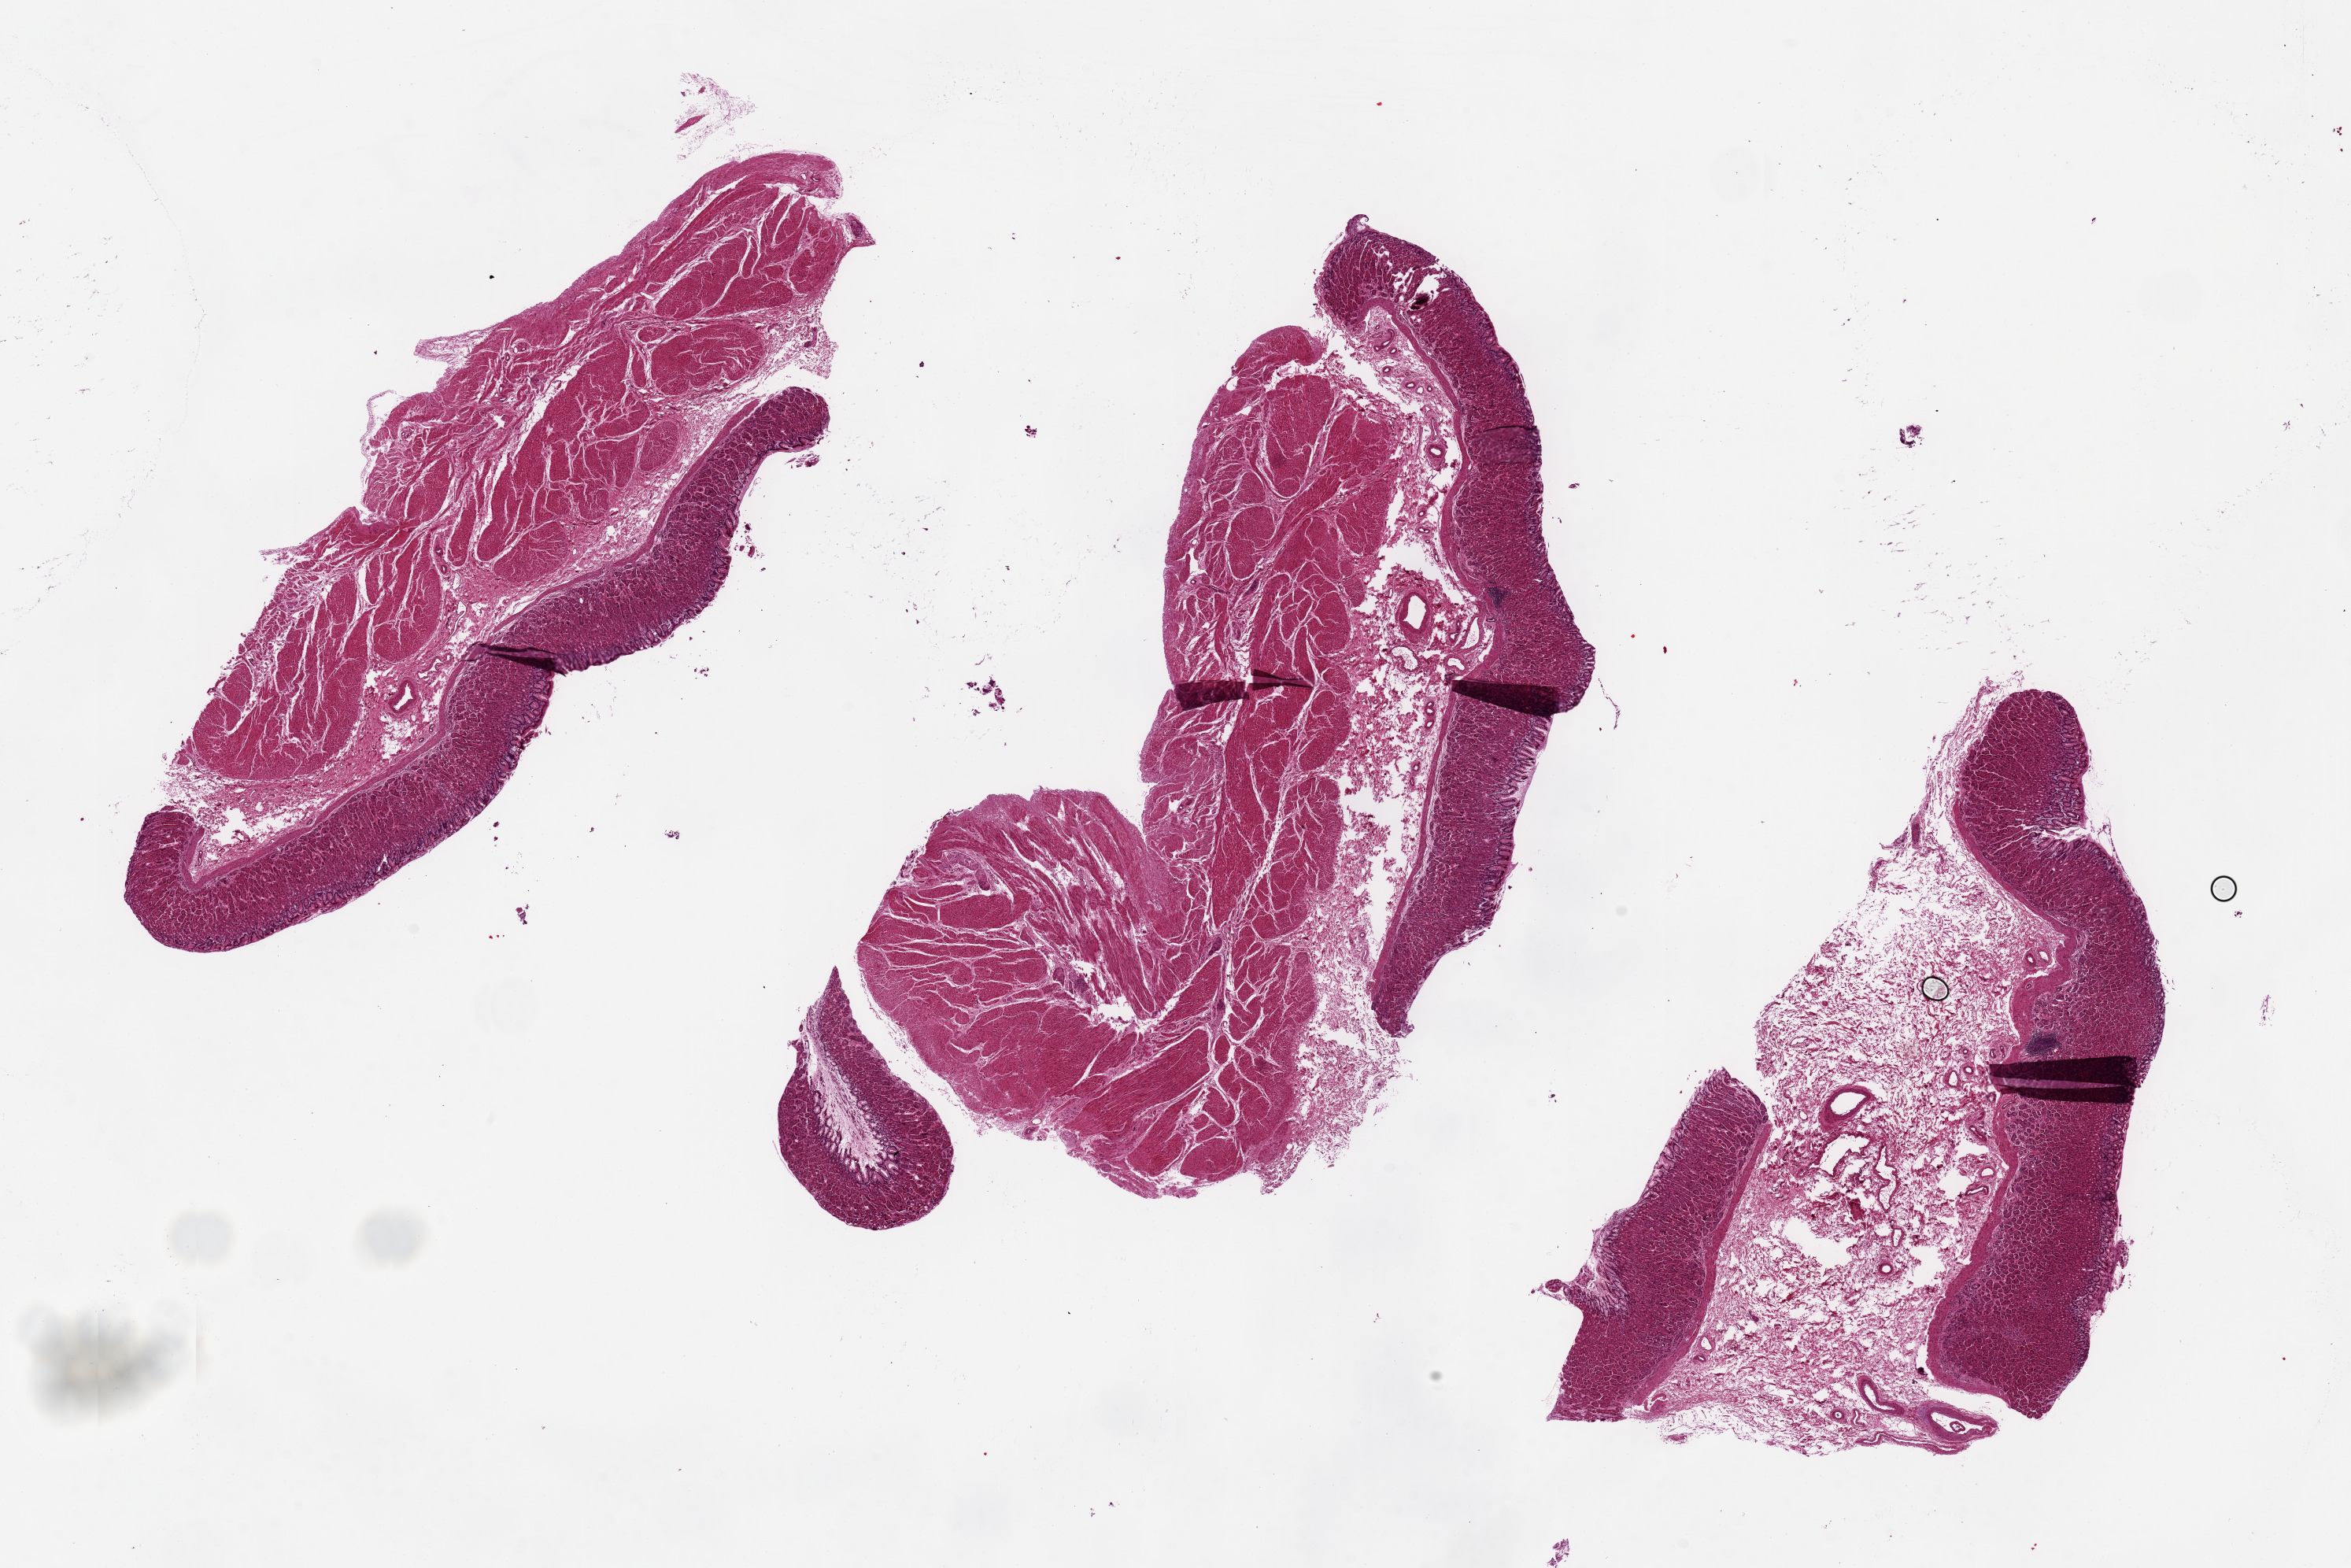
Whole-slide image, hematoxylin and eosin (H&E) stain — a low-resolution overview of the entire scanned area, about 23.6 x 15.8 mm (from a 20x scan), PAXgene-fixed paraffin-embedded (PFPE) section, target tissue: stomach, tissue donor sample. Donor sex: male.
• review note (as recorded): Remarkably well preserved; single focus lymphocytic gastritis